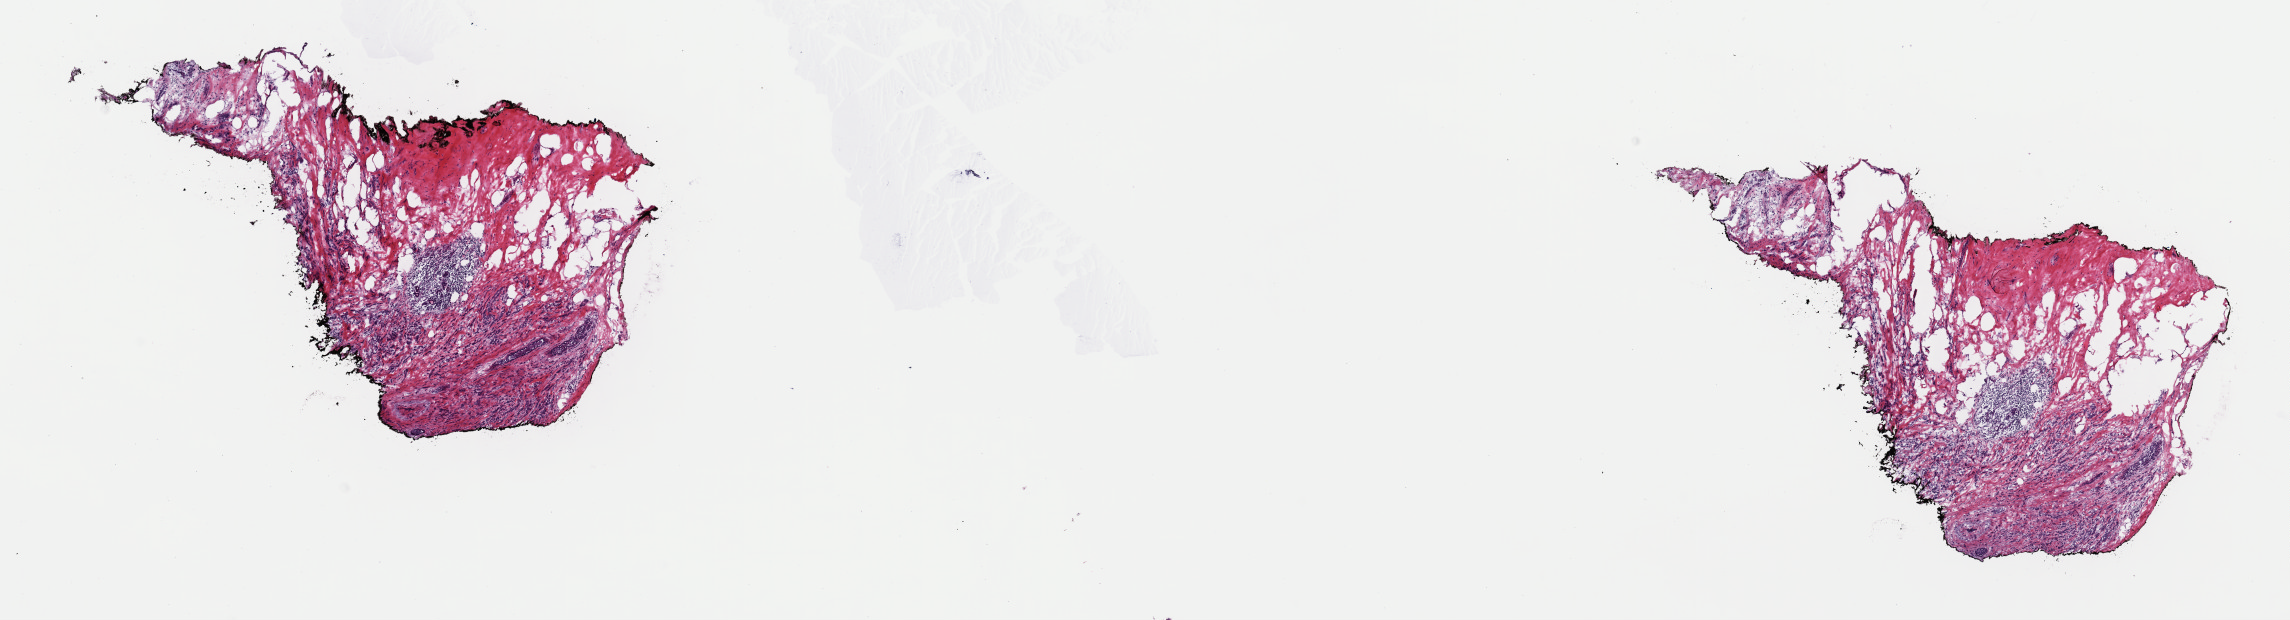
Digitized Hematoxylin and eosin (H&E) stained tissue section (whole slide), whole scanned area (about 18.1 x 4.9 mm, slide scanned at 40x) shown as a low-resolution overview. Frozen section from the top of the tissue portion. Breast, primary tumour sample. Female patient; age at initial diagnosis 79 years. Pathologist review of this section (percent, as recorded): tumour cells 50%, tumour nuclei 60%, normal cells 50%, stromal cells 0%, necrosis 0%. Infiltration values recorded for this section: lymphocyte infiltration 10%, monocyte infiltration 0%, neutrophil infiltration 0%.
Lymph nodes positive (case pathology): 1 of 2 examined. Histologic diagnosis: Lobular carcinoma, NOS. AJCC pathologic stage: IIB (7th edition).